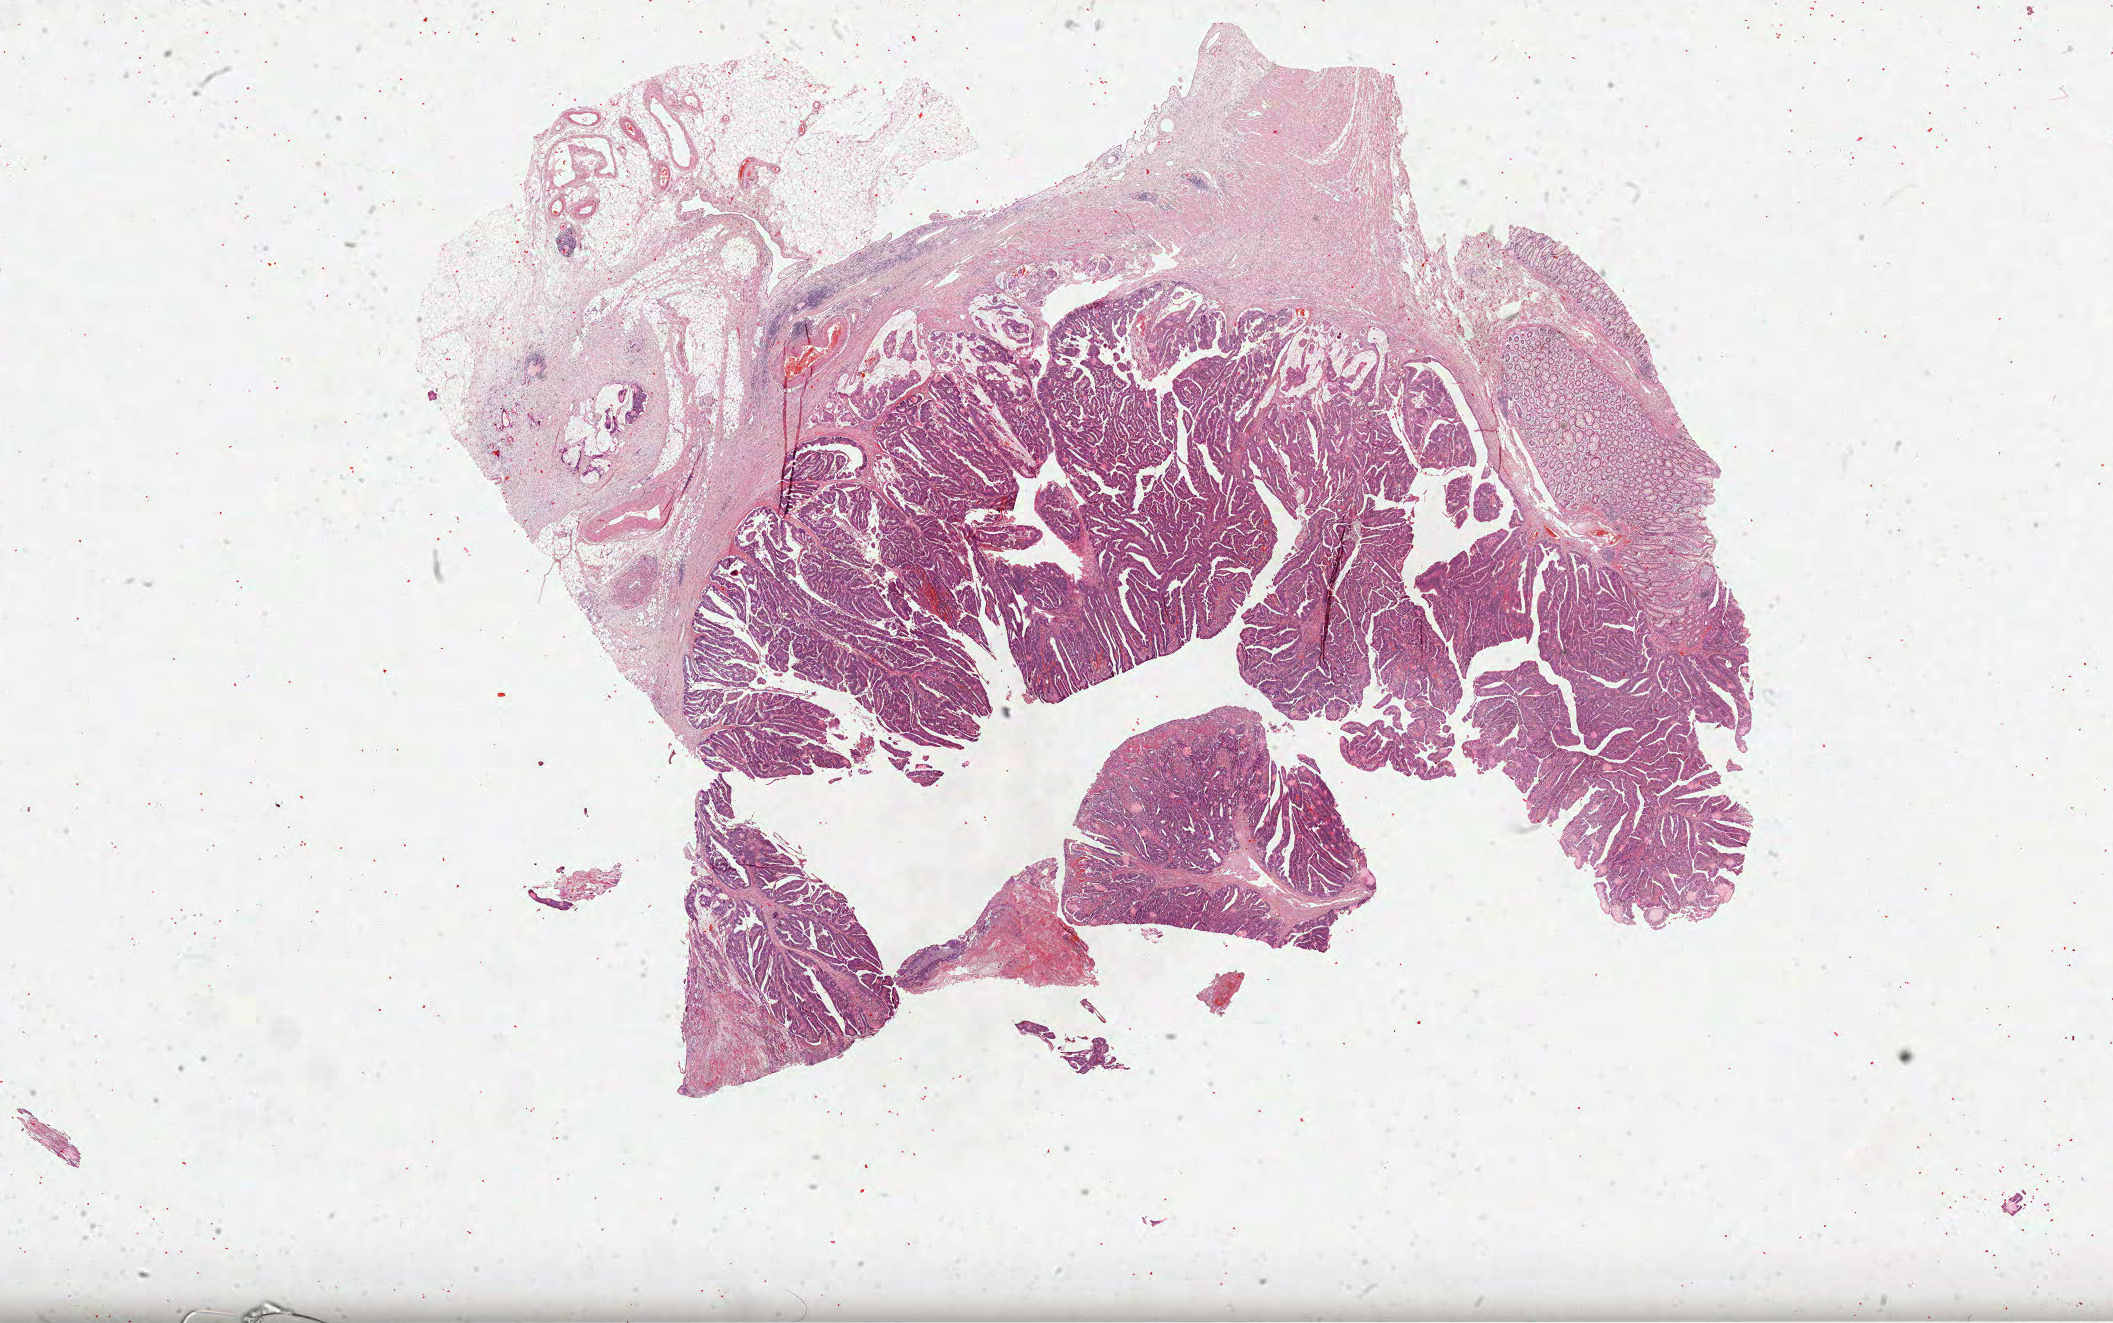
Whole-slide histology image, H&E — a low-resolution overview of the entire scanned area, about 34.1 x 21.3 mm (slide scanned at 40x); formalin-fixed paraffin-embedded (FFPE) diagnostic section; primary tumour sample from the colon. Female patient; age at initial diagnosis 79 years.
Pathologic diagnosis: Adenocarcinoma, NOS (hepatic flexure of colon).